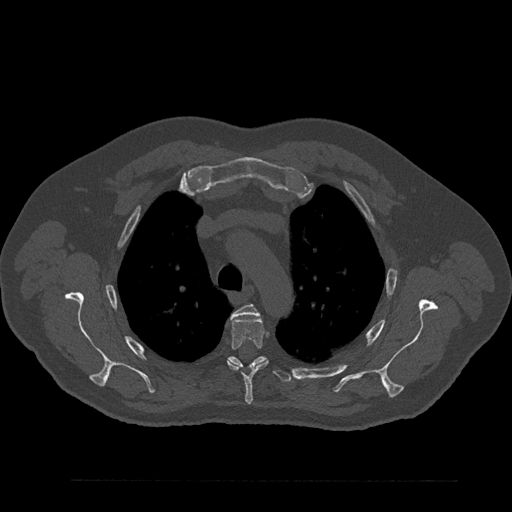
CT including the spine, one axial slice. Position 636 of 797 along the scan axis. Reconstruction kernel Br40s/3. 120 kVp. Bone window (W 1800 / L 400 HU). 0.5 mm slice thickness. 512 × 512 image matrix, field of view 430 × 430 mm. Patient: male, 61 years. Case-level facts recorded for this patient, not image findings: primary cancer: prostate.
Structures marked on this image (semi-automatically segmented with operator editing):
- T3 vertebra: bounding box [x1, y1, x2, y2] px = [230, 304, 259, 318]
- T4 vertebra: [227, 317, 268, 405]
- T5 vertebra: [228, 356, 291, 383]